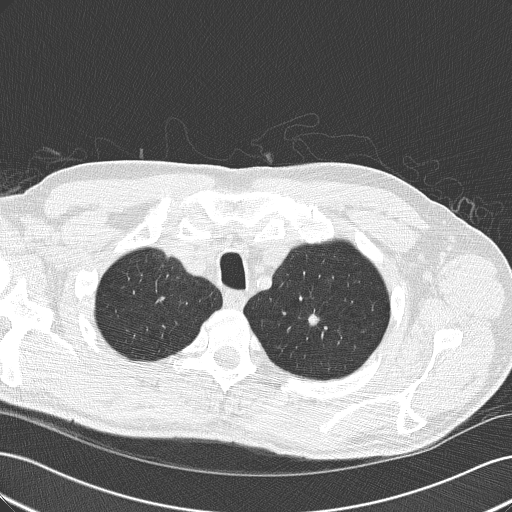
Low-dose screening chest CT, axial slice, third annual screen, lung window (W 1500 / L -600 HU), 512 × 512 image matrix, field of view 360 × 360 mm. Male participant, aged 64 years at enrolment.
• Lesion marked by an expert reader, bounding box (x1, y1, x2, y2) in pixels: (289, 299, 334, 343).
• The exam's reader record, not a measurement of the box and not confirmed to be the same lesion: non-calcified nodule or mass ≥4 mm, left upper lobe, 8 × 8 mm, smooth margins, soft tissue attenuation, pre-existing on the prior screen: yes; interval growth: yes.
• Participant outcome: lung cancer diagnosed 111 days after this screen — adenocarcinoma, NOS, left upper lobe, poorly differentiated (G3), stage IA (AJCC 6th edition), 10 mm at pathology.